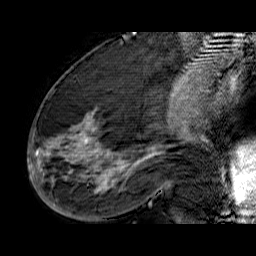
Breast MRI (dynamic contrast-enhanced), one sagittal slice. Slice 30 of 60 in the series (ordered by position). Dynamic contrast-enhanced series, time point 2 of 6 at this slice position (early post-contrast). 1.5 T. TE 6.5 ms, TR 32.9 ms. 4 mm slice thickness. 256 × 256 image matrix, field of view 200 × 200 mm. Female patient. From the clinical record (not read from this slice): setting: breast cancer imaged before/during neoadjuvant chemotherapy; receptor status: HR-positive, HER2-negative.
Outlined on this slice (semi-automatically segmented with operator editing):
- analysis volume of interest (the breast-tissue region the enhancement analysis was run in; not a lesion): bounding box <33,74,176,210> (left, top, right, bottom; pixels)
- tumour enhancement mask (voxels above the 100 % enhancement threshold inside the analysis volume of interest): <33,109,167,194>